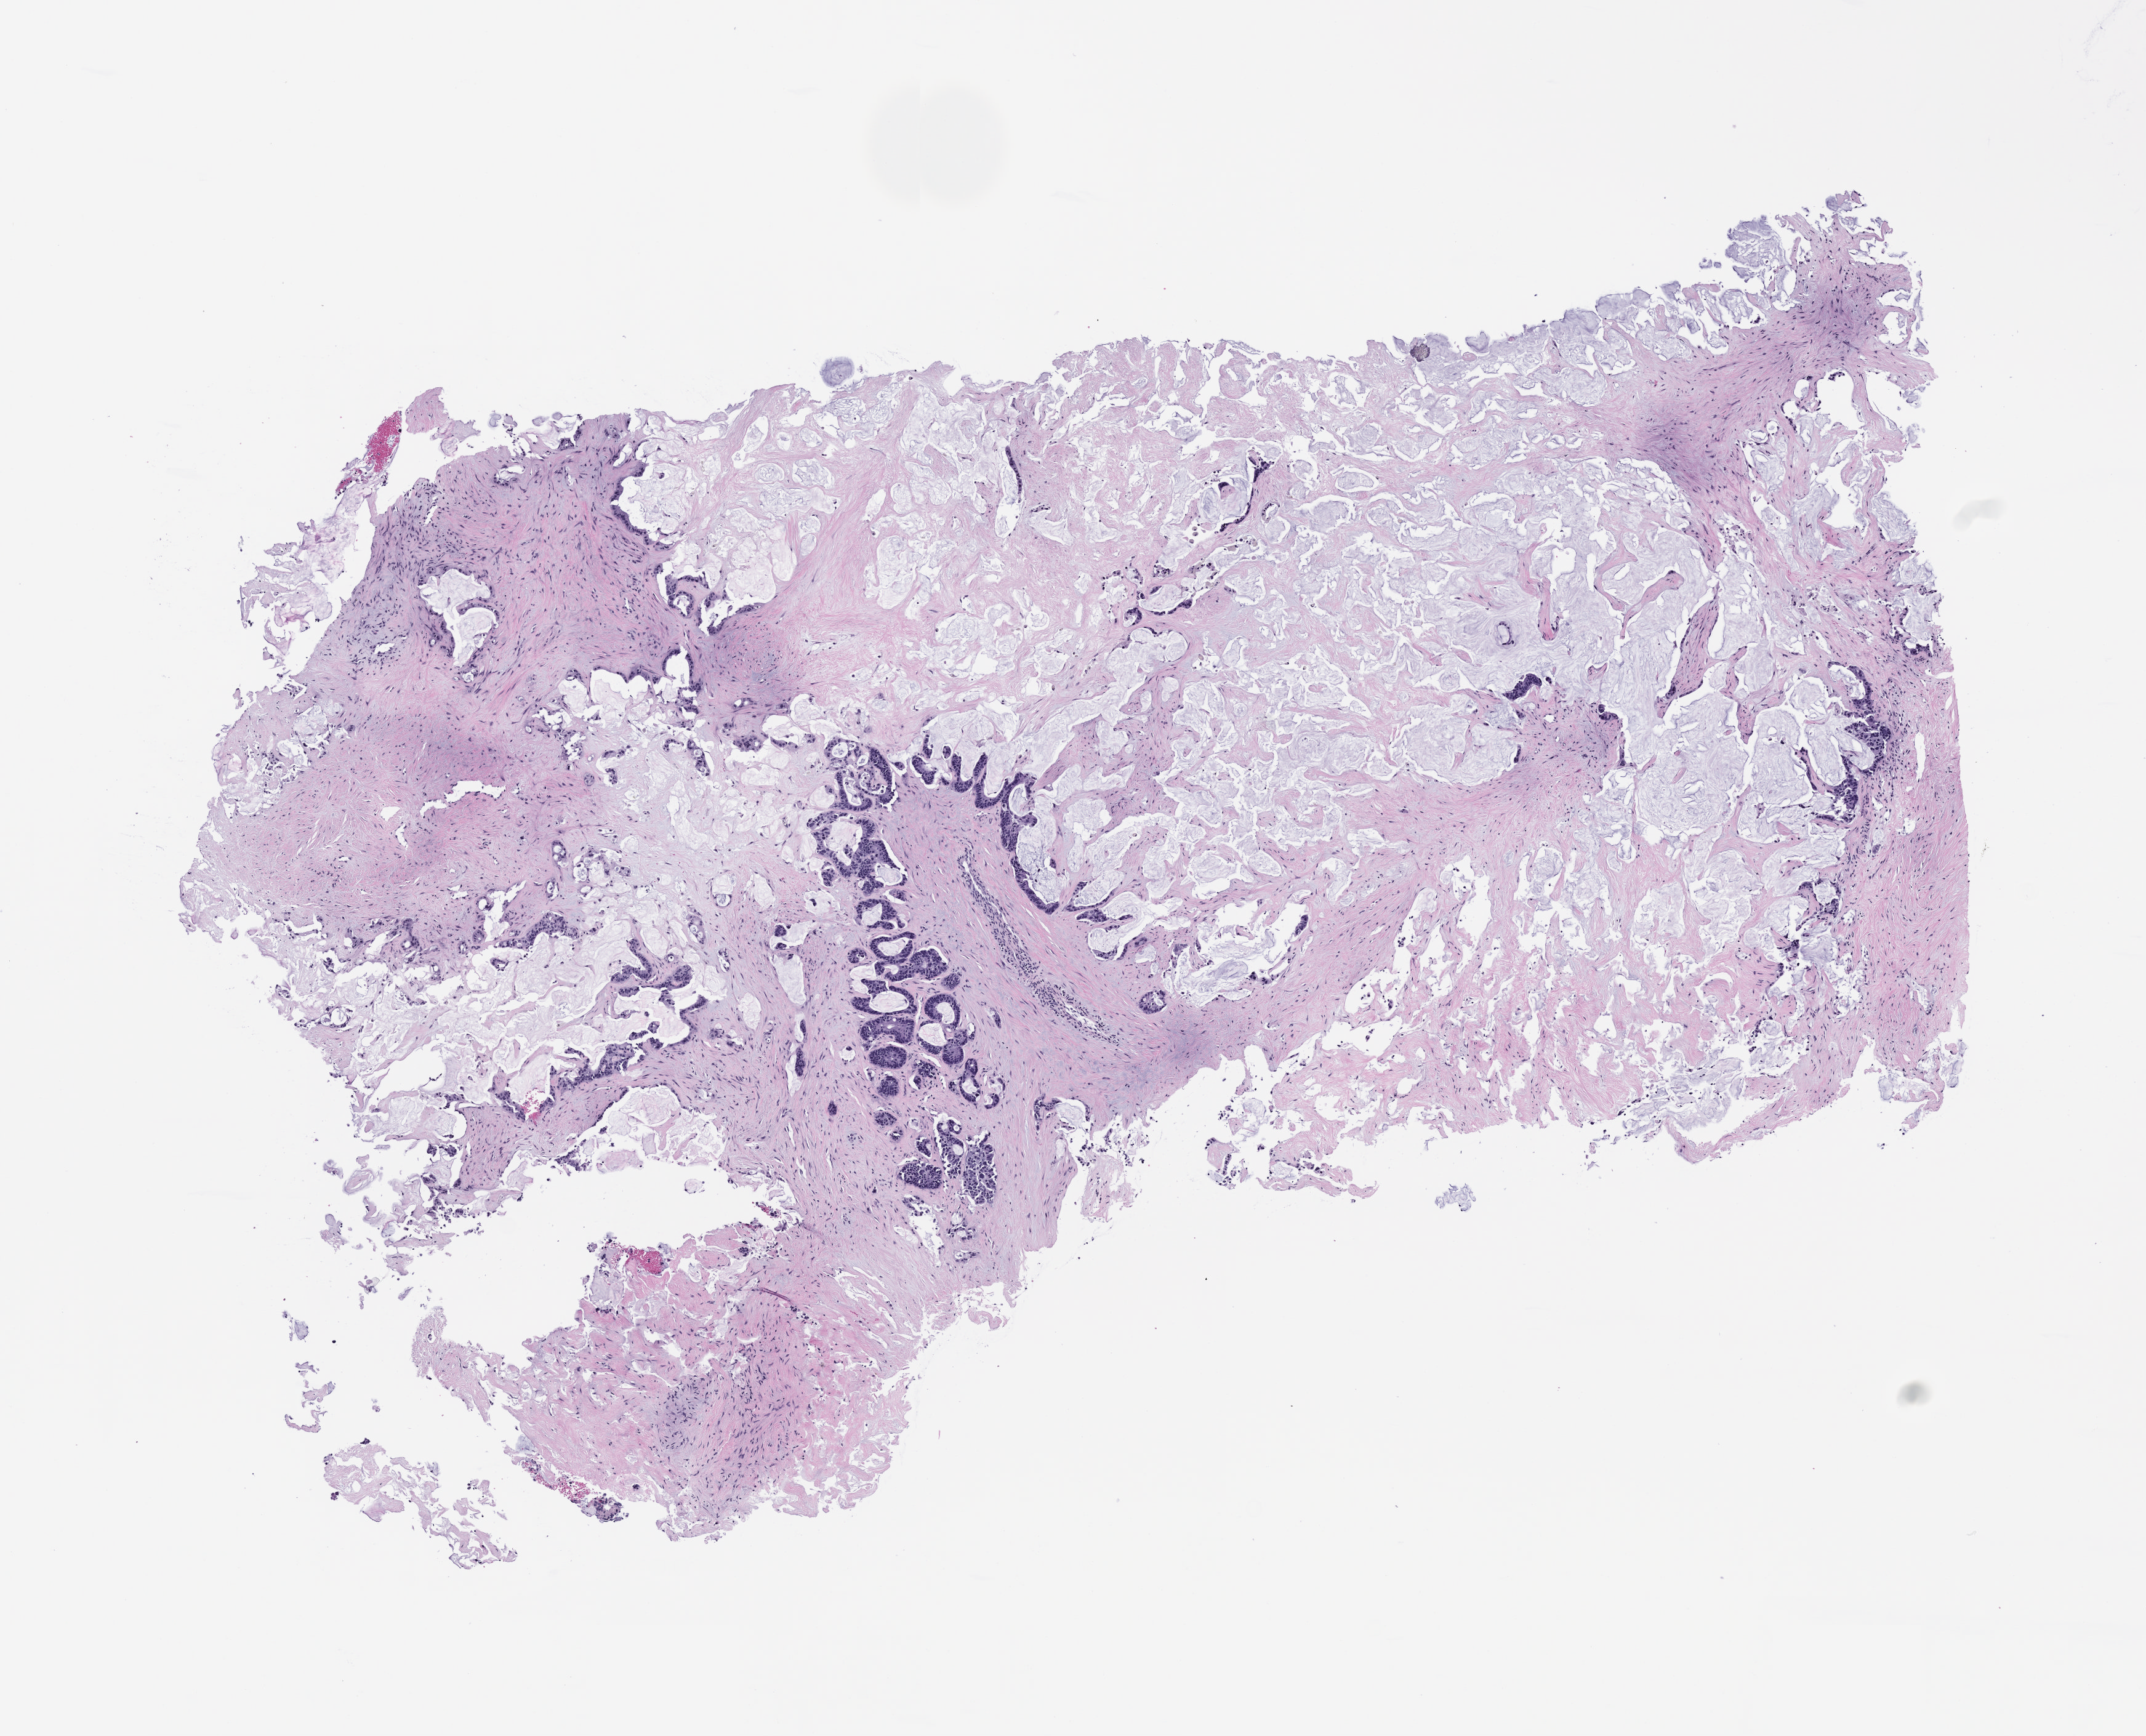
Whole-slide image, hematoxylin and eosin (H&E) stain of the patient's (originator) tumor tissue — whole scanned area (about 7.0 x 5.7 mm) shown as a low-resolution overview, FFPE section, originating tumor site category: rectum. Patient: male.
Diagnosis: Rectal Adenocarcinoma.